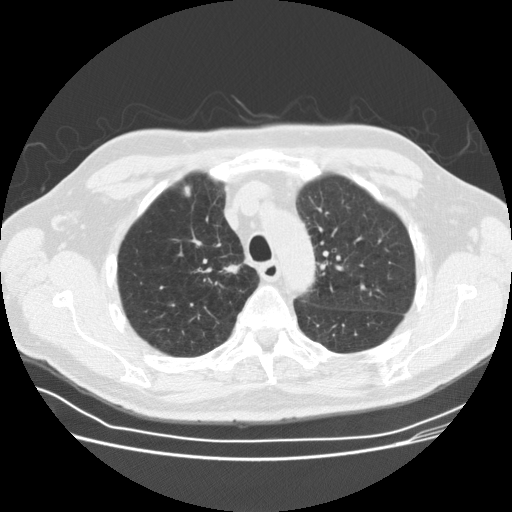
Chest CT (low-dose screening protocol), one axial image, third screening round (two years after baseline), lung window (W 1500 / L -600 HU), 2.5 mm slice thickness, 120 kVp, slice 122 of 164 in the series, 512 × 512 image matrix. Male, age 69 years at enrolment. Current smoker at enrolment.
• Expert-annotated lung lesion, box from (x=221, y=256) to (x=259, y=288) px.
• The exam's reader record, not a measurement of the box and not confirmed to be the same lesion: non-calcified nodule or mass ≥4 mm, right upper lobe, 12 × 10 mm, spiculated (stellate) margins, soft tissue attenuation, pre-existing on the prior screen: yes; interval growth: yes.
• Official screen result: positive, other.
• Participant outcome: lung cancer diagnosed 36 days after this screen — squamous cell carcinoma, NOS, right upper lobe, moderately differentiated (G2), stage IA (AJCC 6th edition), 9 mm at pathology.